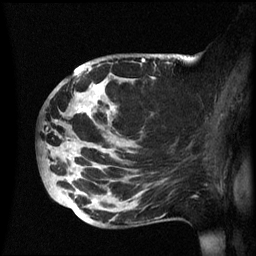
Breast MRI (dynamic contrast-enhanced), one sagittal slice. Dynamic contrast-enhanced series, image 2 of 3 at this slice position (ordered by acquisition). 1.5 T. TE 4.2 ms, TR 8.4 ms. 2.4 mm slice thickness. 256 × 256 image matrix. Female patient, age 49 years.
Structures marked on this image (semi-automatic segmentation, software-assisted and operator-edited):
- analysis volume of interest (the breast-tissue region the enhancement analysis was run in; not a lesion): bounding box (x1, y1, x2, y2) in pixels: (40, 54, 174, 228)
- tumour enhancement mask (voxels above the 70 % enhancement threshold inside the analysis volume of interest): (78, 60, 152, 168)